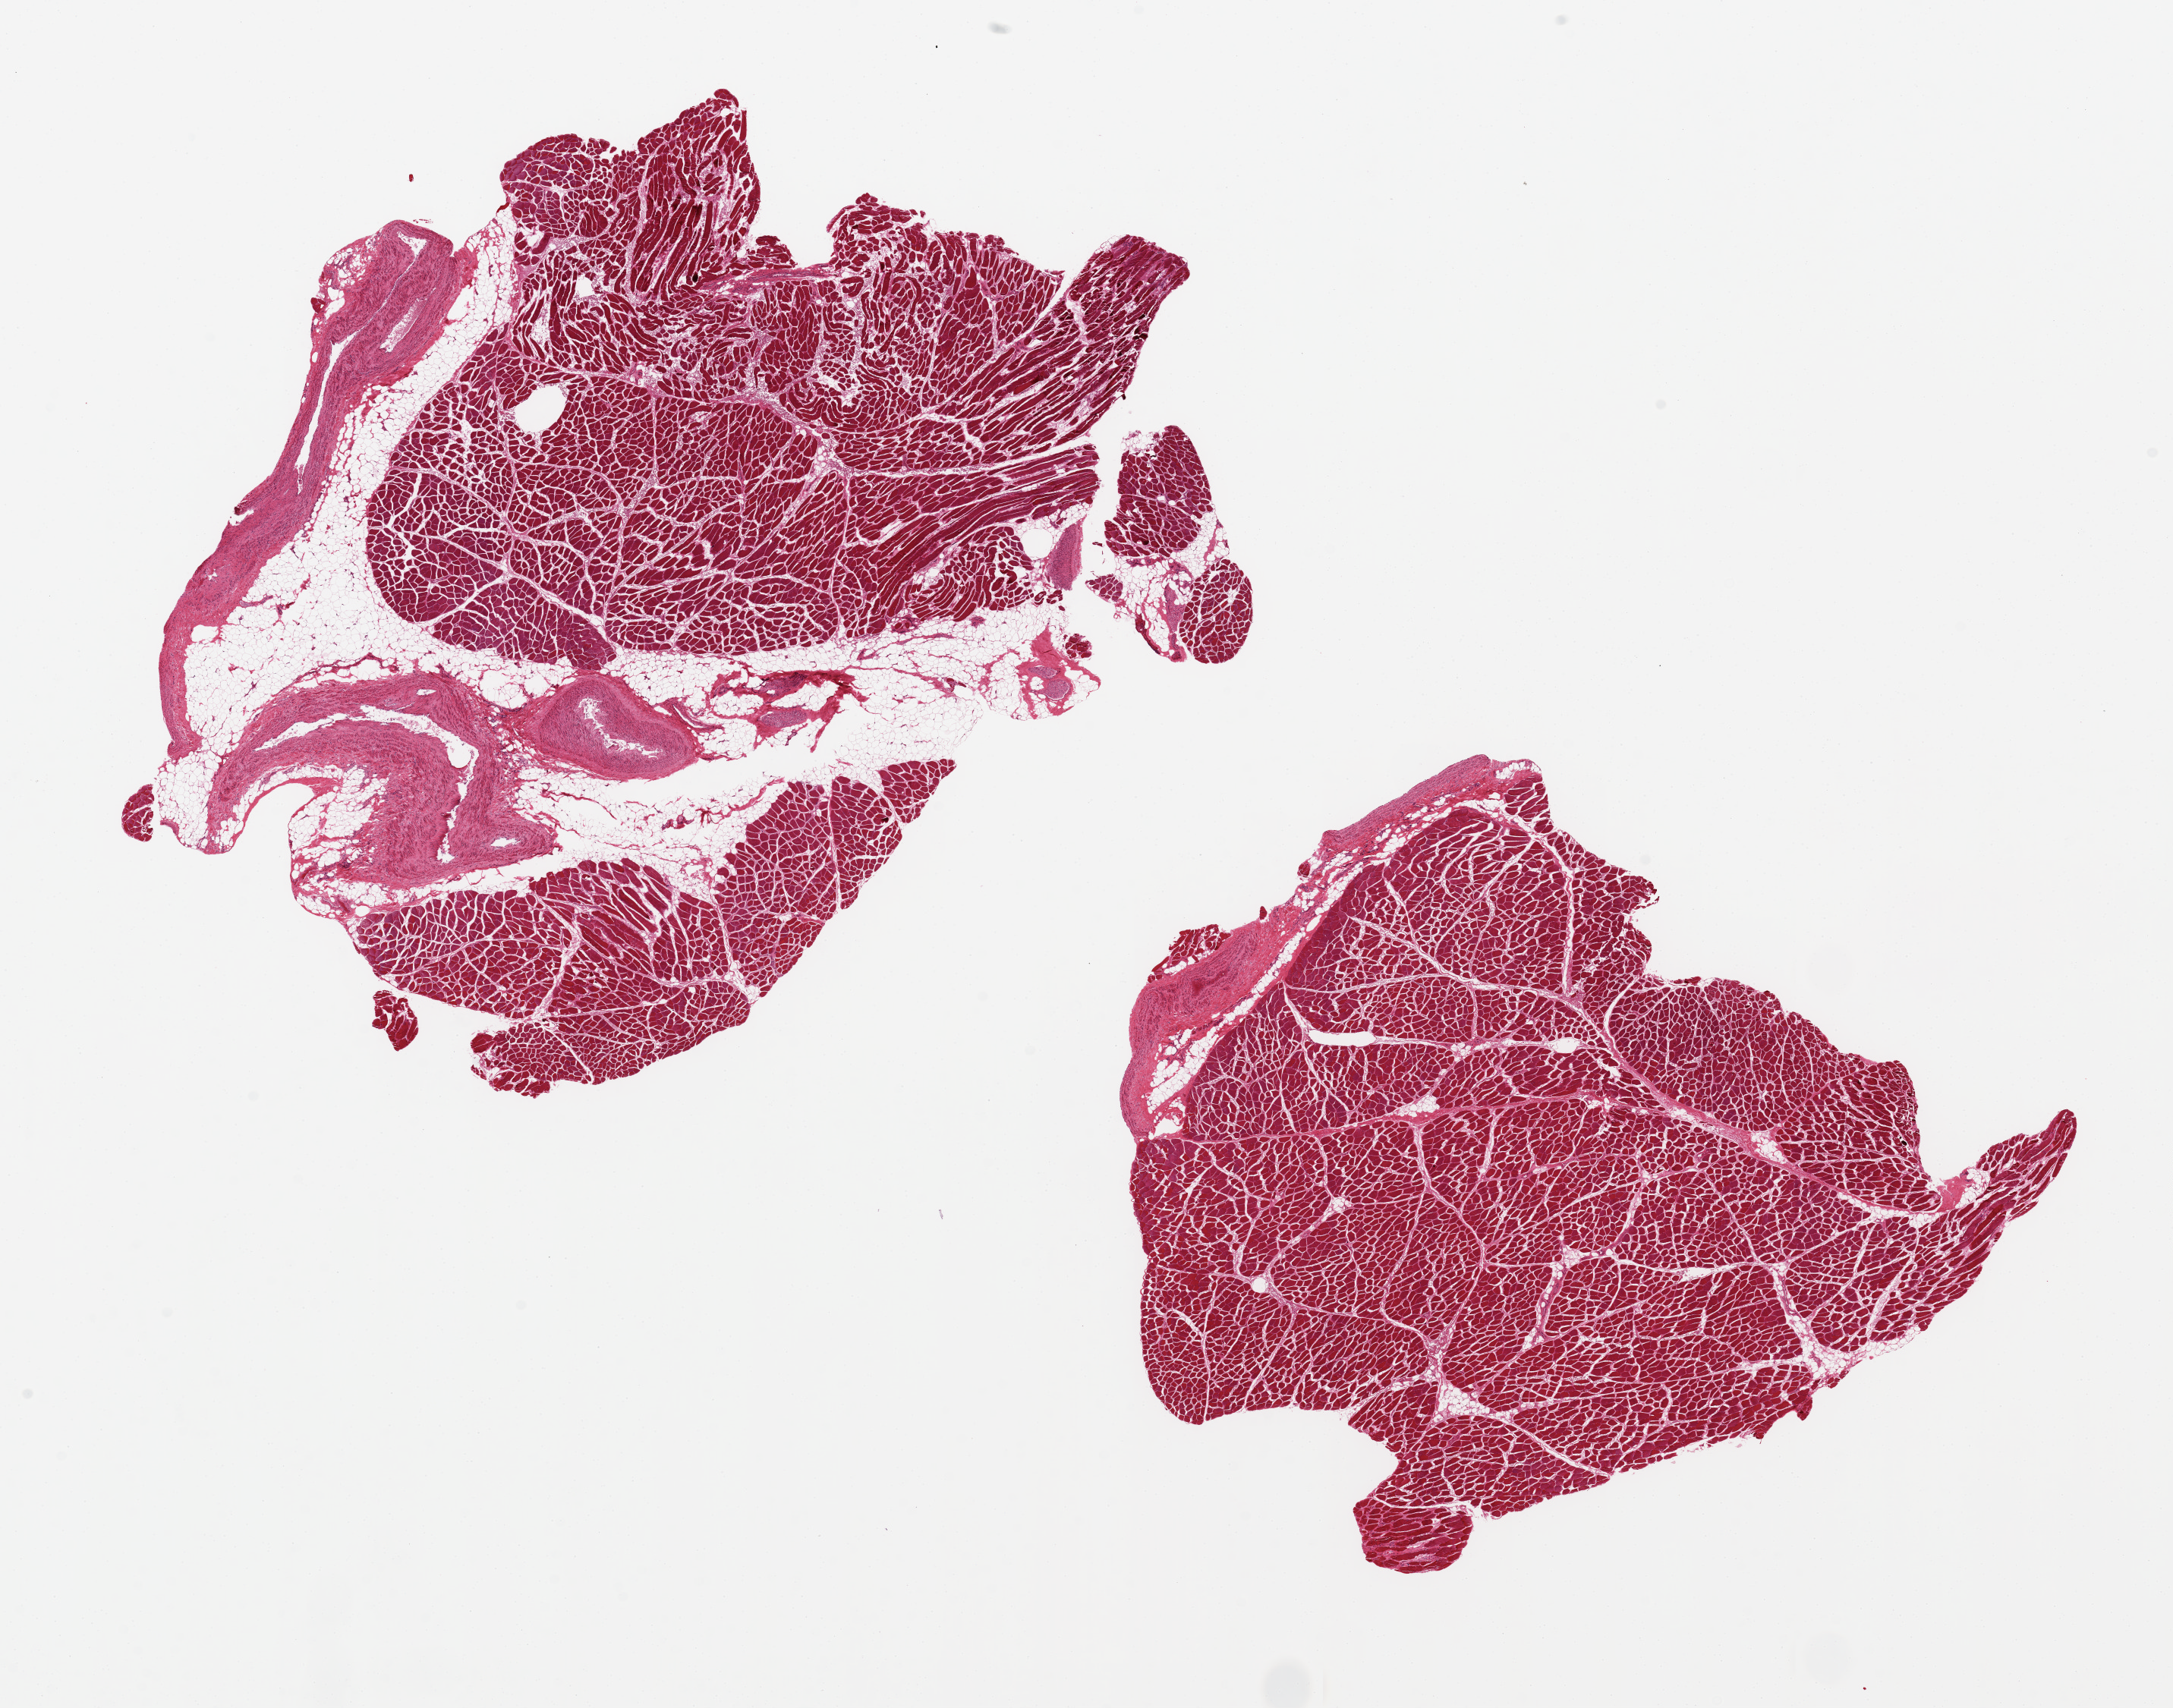
Digitized haematoxylin and eosin-stained section, brightfield, shown as a low-resolution overview of the whole scanned area (about 22.6 x 17.8 mm); PAXgene-fixed, paraffin-embedded tissue; target tissue: skeletal muscle; tissue donor sample. Donor sex: male.
Review note (as recorded): 2 pieces, 10x7 && 8x7 mm; larger piece has attached veins & adipose tissue, ~30%.